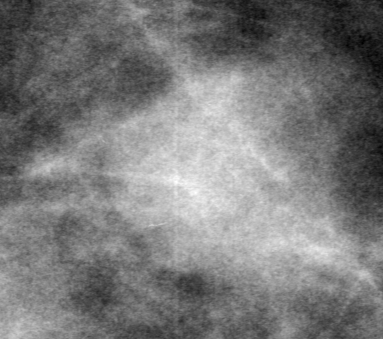
Crop from a digitized film mammogram around one marked abnormality, left breast, CC view, BI-RADS breast density category 2 (scale 1–4).
- Marked abnormality: mass, shape lobulated, margins obscured; BI-RADS assessment category 0 (incomplete: needs additional imaging); pathology result (as recorded, not read from the image): benign.